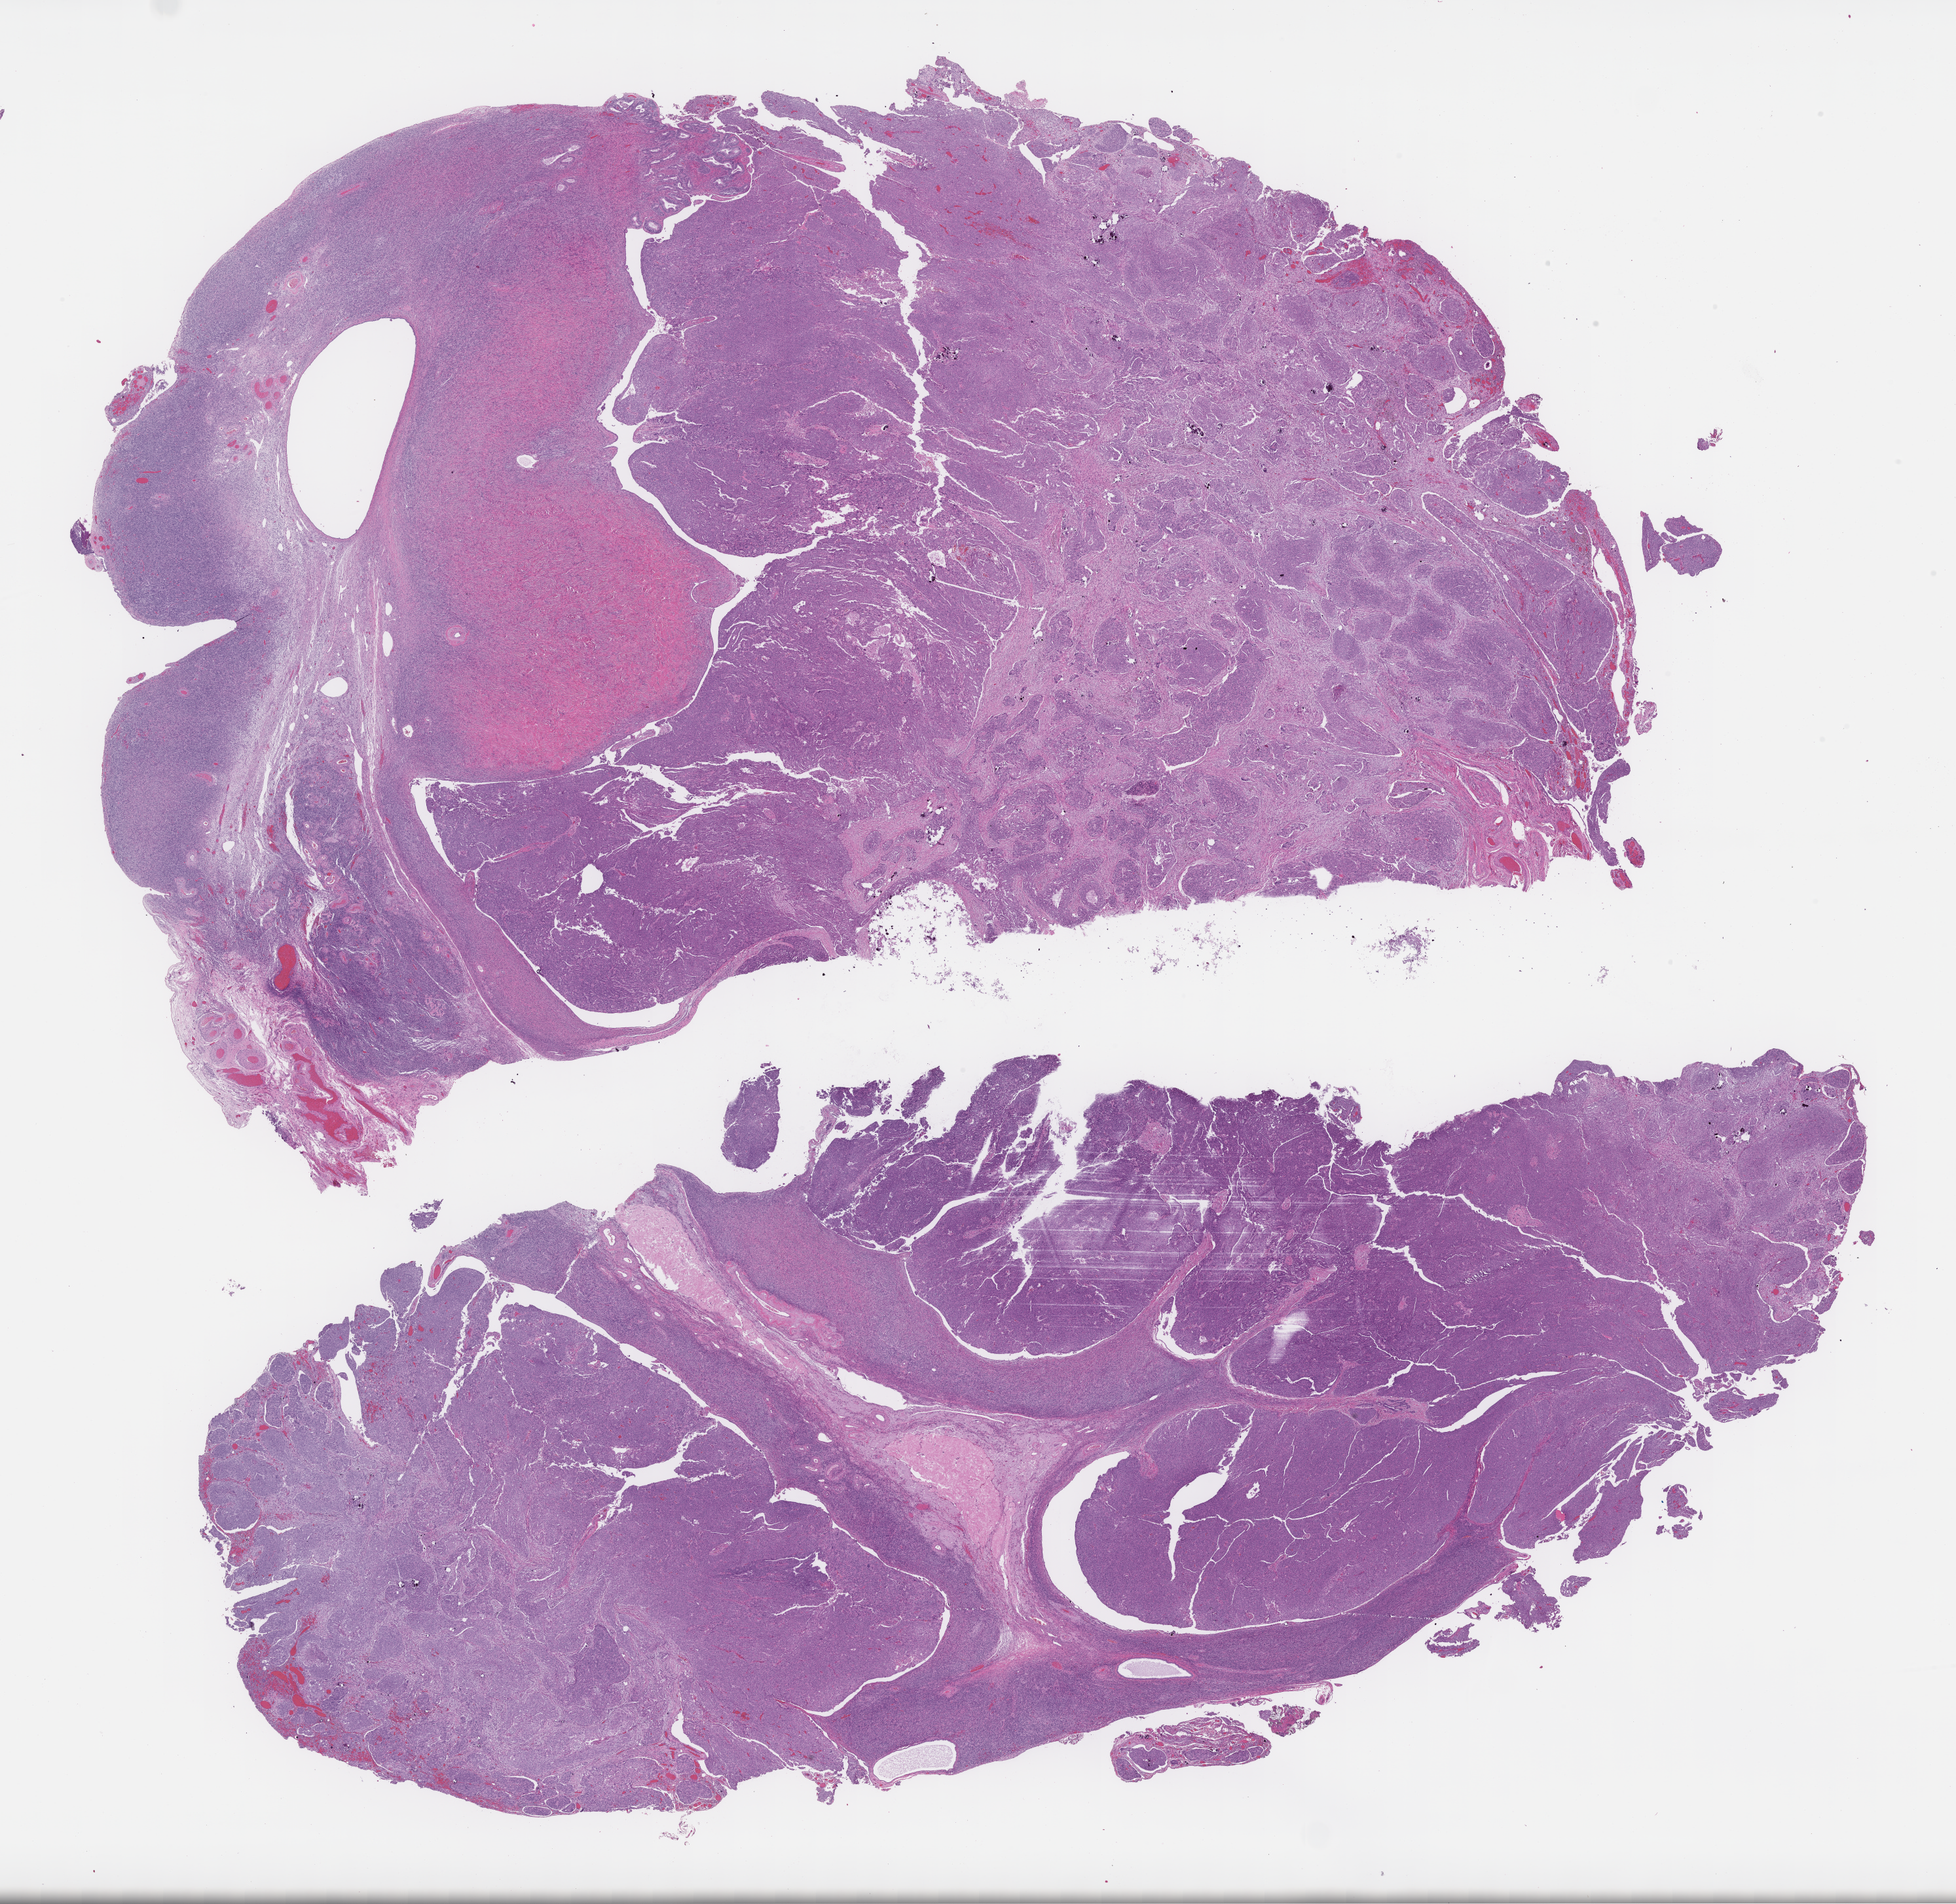
Hematoxylin and eosin (H&E) whole-slide image — shown as a low-resolution overview of the whole scanned area (about 24.1 x 23.5 mm). Formalin-fixed paraffin-embedded section. Site: ovary. Specimen time point: archival tissue. Patient sex: female.
This section: primary tumor. Diagnosis: Ovarian Carcinoma.